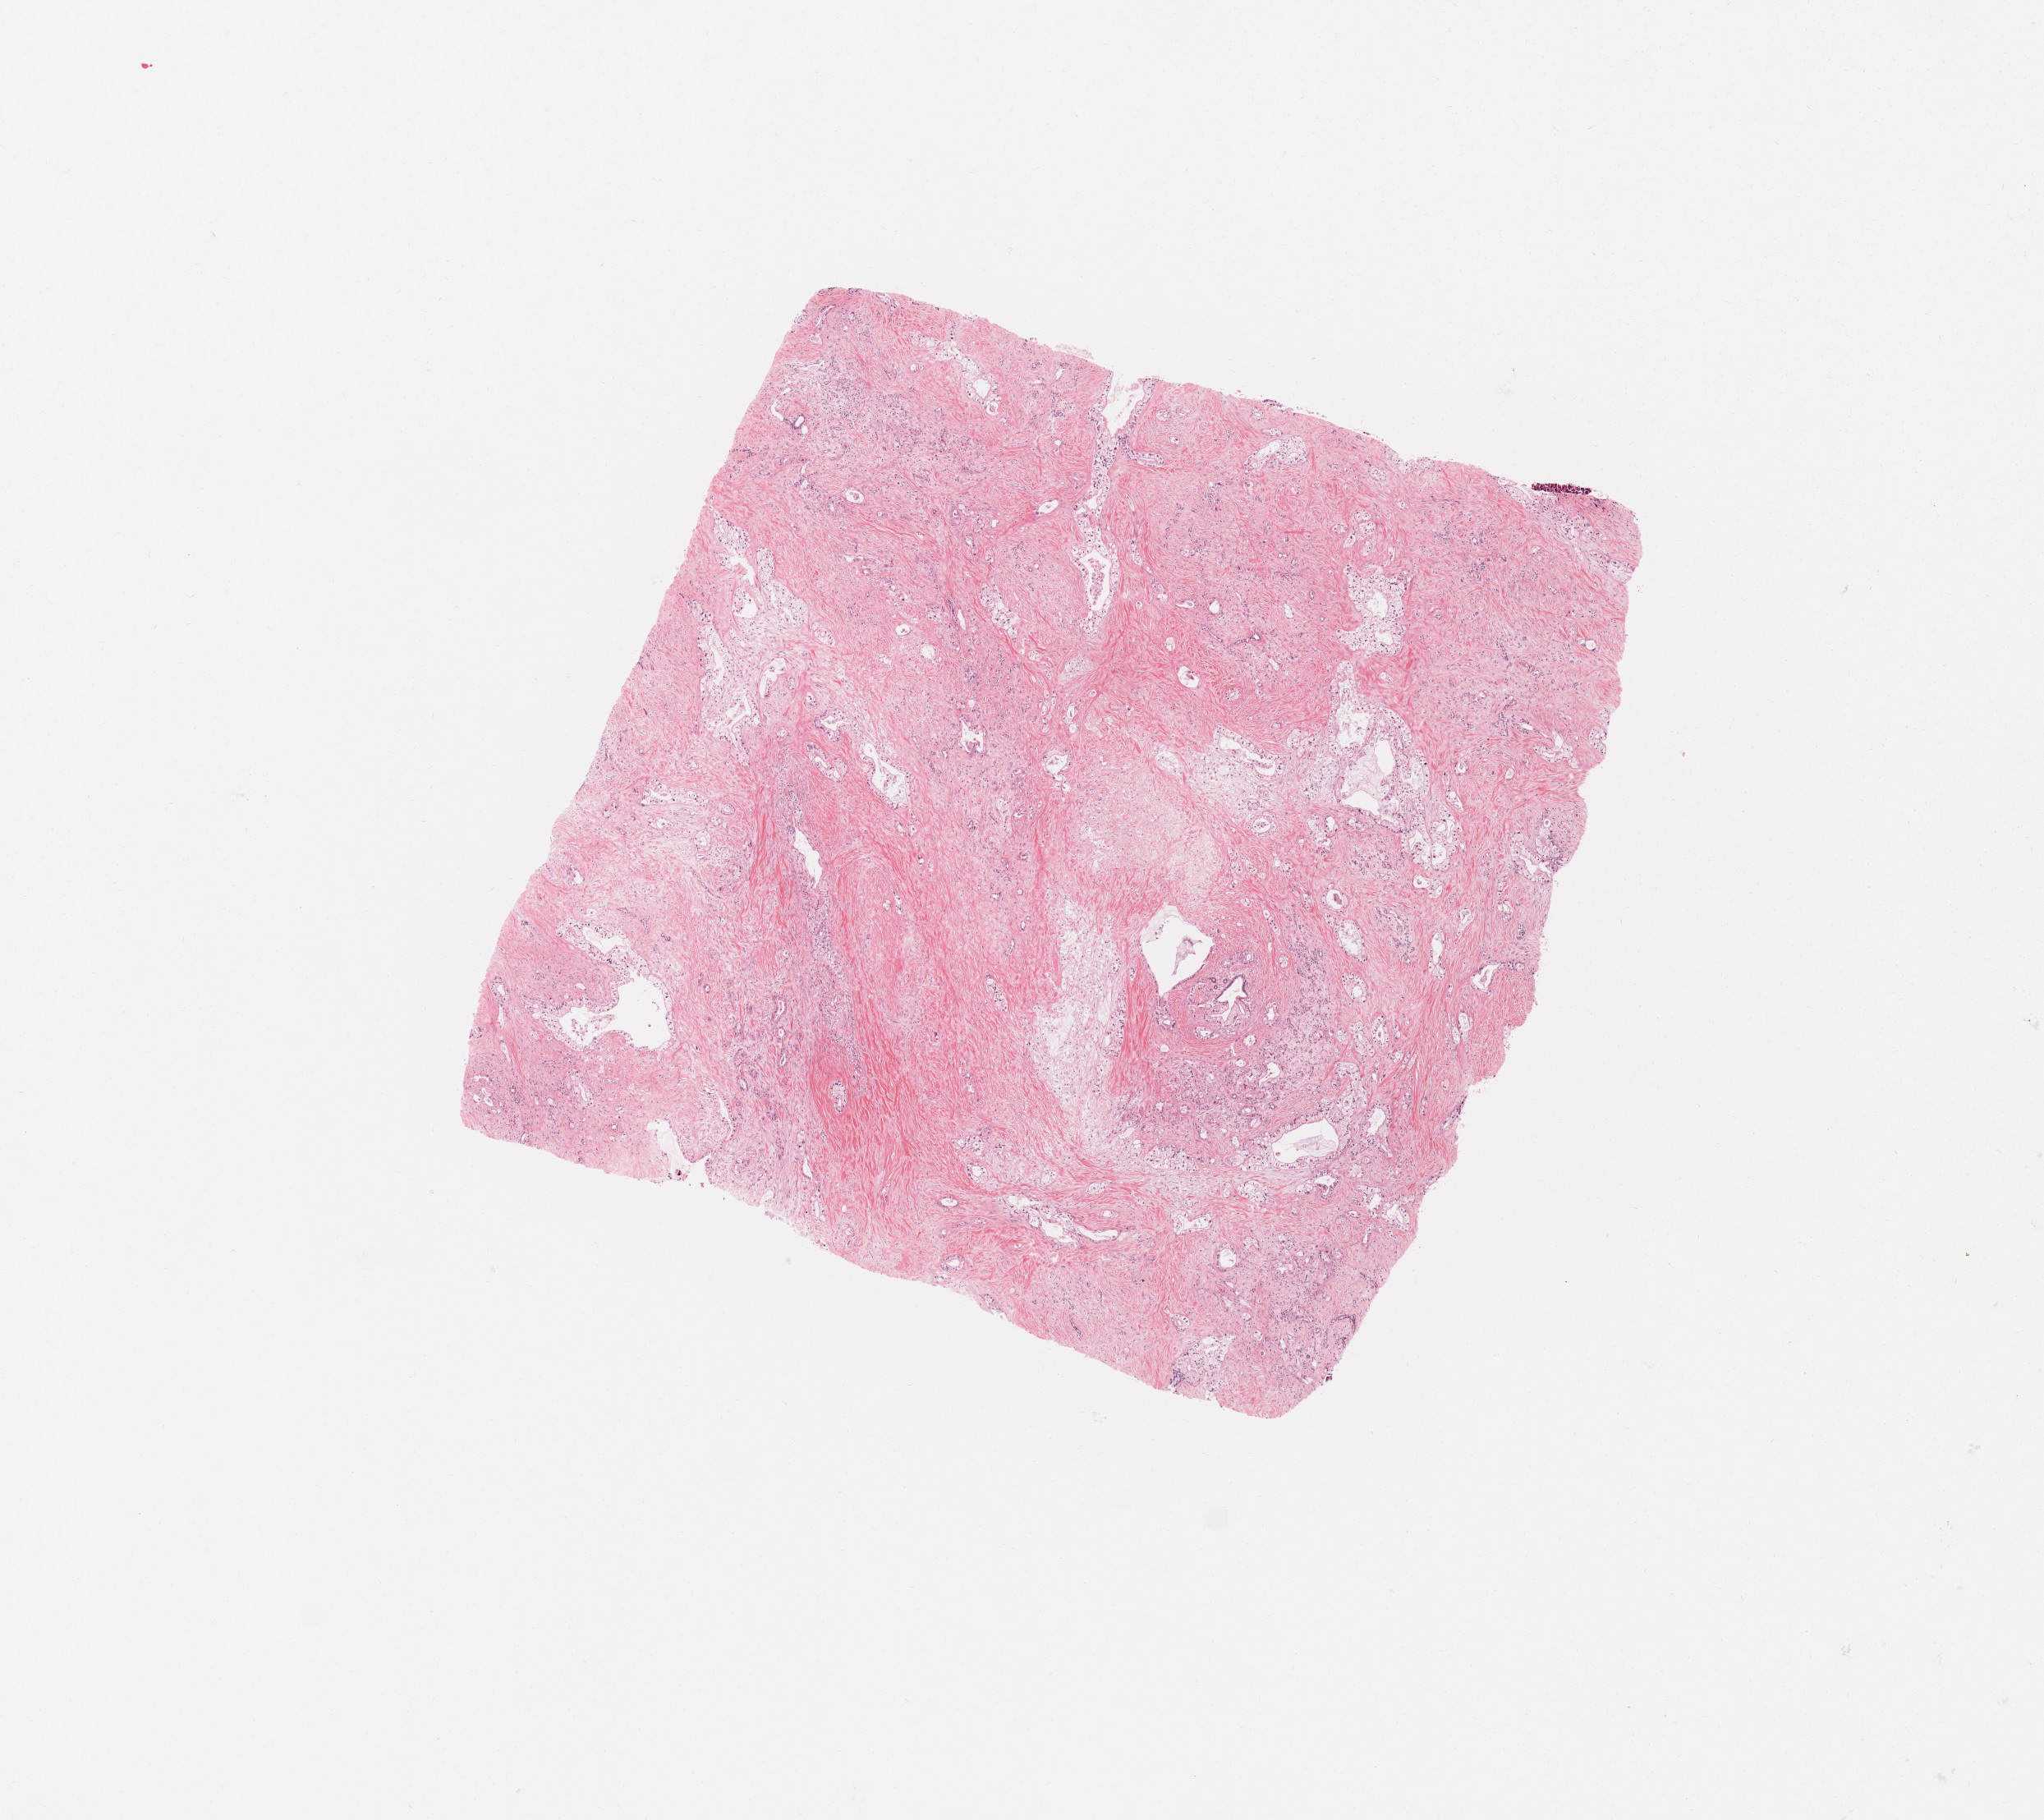
Digitized H&E-stained tissue section (whole slide) — a low-resolution overview of the entire scanned area, about 9.8 x 8.8 mm; tumour tissue sample, sampled site: pancreas. Female, 41 y/o. Histologic grade: G2 (moderately differentiated). Slide review estimates, as recorded: tumour nuclei 30%, necrosis 0%.
- diagnosis: Infiltrating duct carcinoma, NOS
- AJCC pathologic stage: III